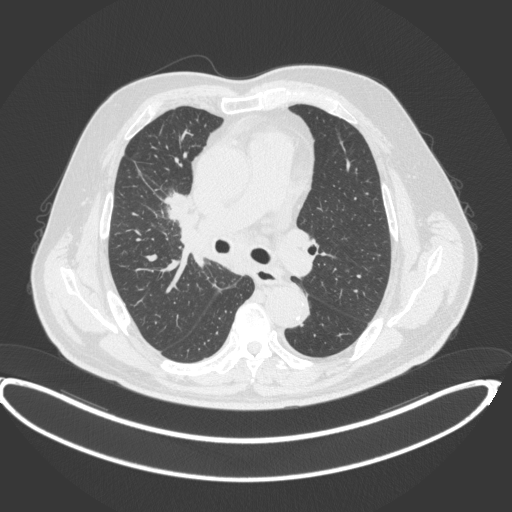
Chest CT, one axial slice; slice 250 of 395 in the series (ordered by position); reconstruction kernel B31f; 120 kVp; lung window (W 1500 / L -600 HU); 1 mm slice thickness; 512 × 512 image matrix, field of view 448 × 448 mm. Patient: male, 62 years. From the clinical record (not read from this slice): clinical TNM (as recorded): T1c N3 M1c.
Structures marked on this image (bounding box drawn by a radiologist):
- lung tumour (recorded histology: adenocarcinoma): bounding box [x1, y1, x2, y2] px = [162, 184, 195, 225]